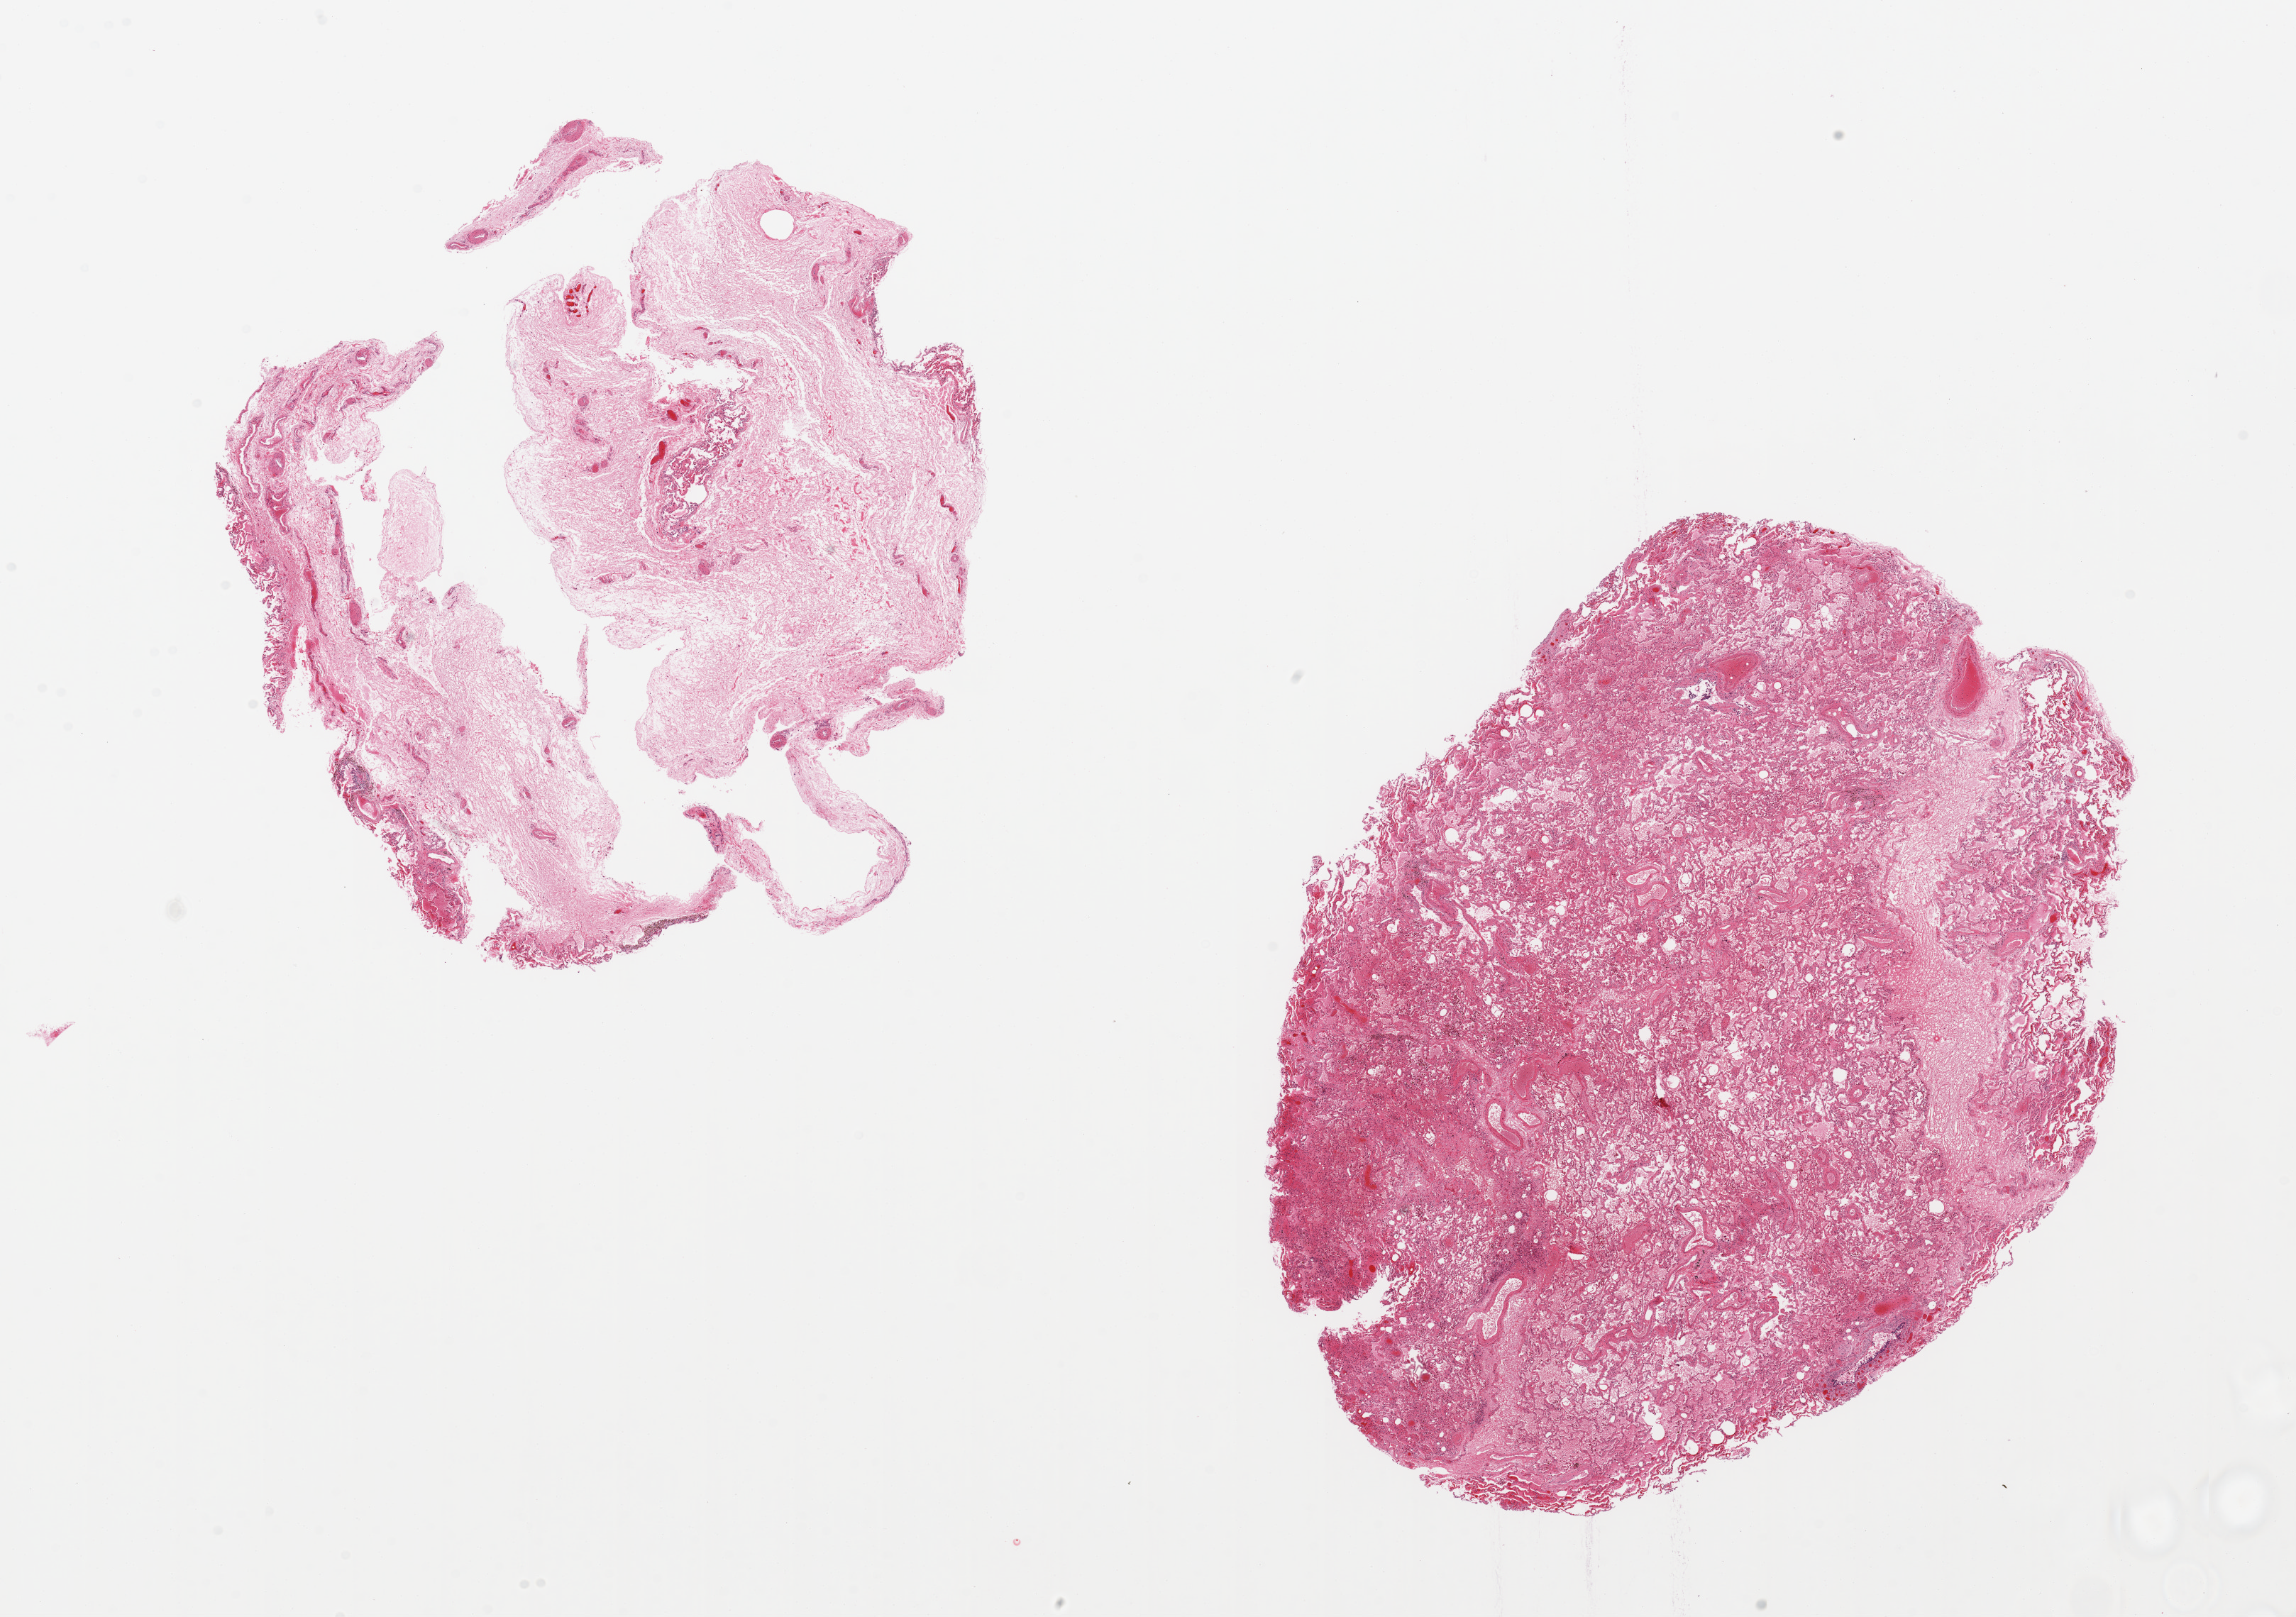
Whole-slide image, H&E stain — whole scanned area (about 25.6 x 18.0 mm) shown as a low-resolution overview; PAXgene-fixed paraffin-embedded (PFPE) section; sampled site (target tissue): lung; tissue donor sample. Donor sex: male.
Reviewer comment on this tissue sample: 2 pieces, one piece 90% necrotic/autolyzed, second shows marked congestion and hemorrhage.